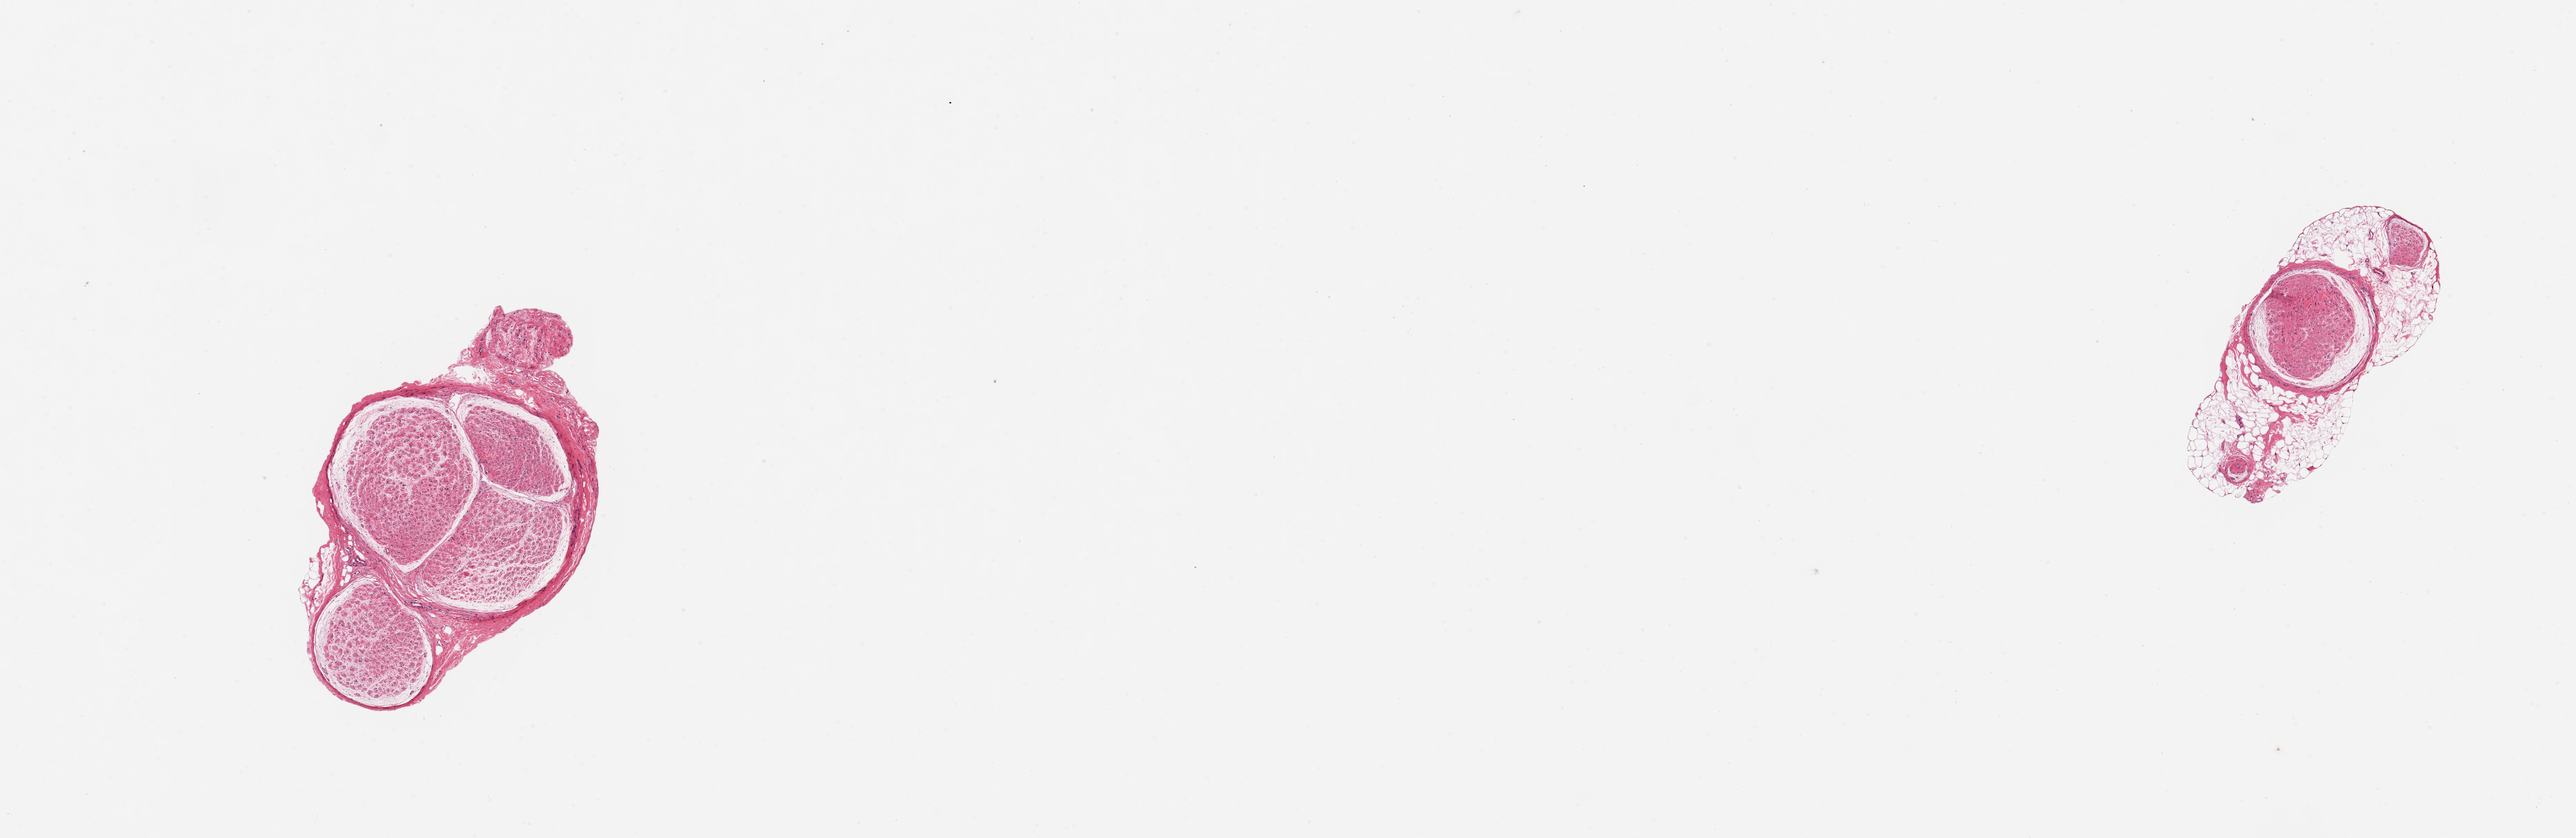
Hematoxylin and eosin (H&E) whole-slide image, low-resolution overview of the scanned area, about 14.8 x 4.8 mm (from a 20x scan); PAXgene-fixed paraffin-embedded (PFPE) section; section of tibial nerve (target tissue); tissue donor sample. Female donor.
Reviewer comment on this tissue sample: 2 pieces, 1.5x2.5mm & 2x1 mm; consists of nerves not artery, the smaller piece encased in ~60% adipose.